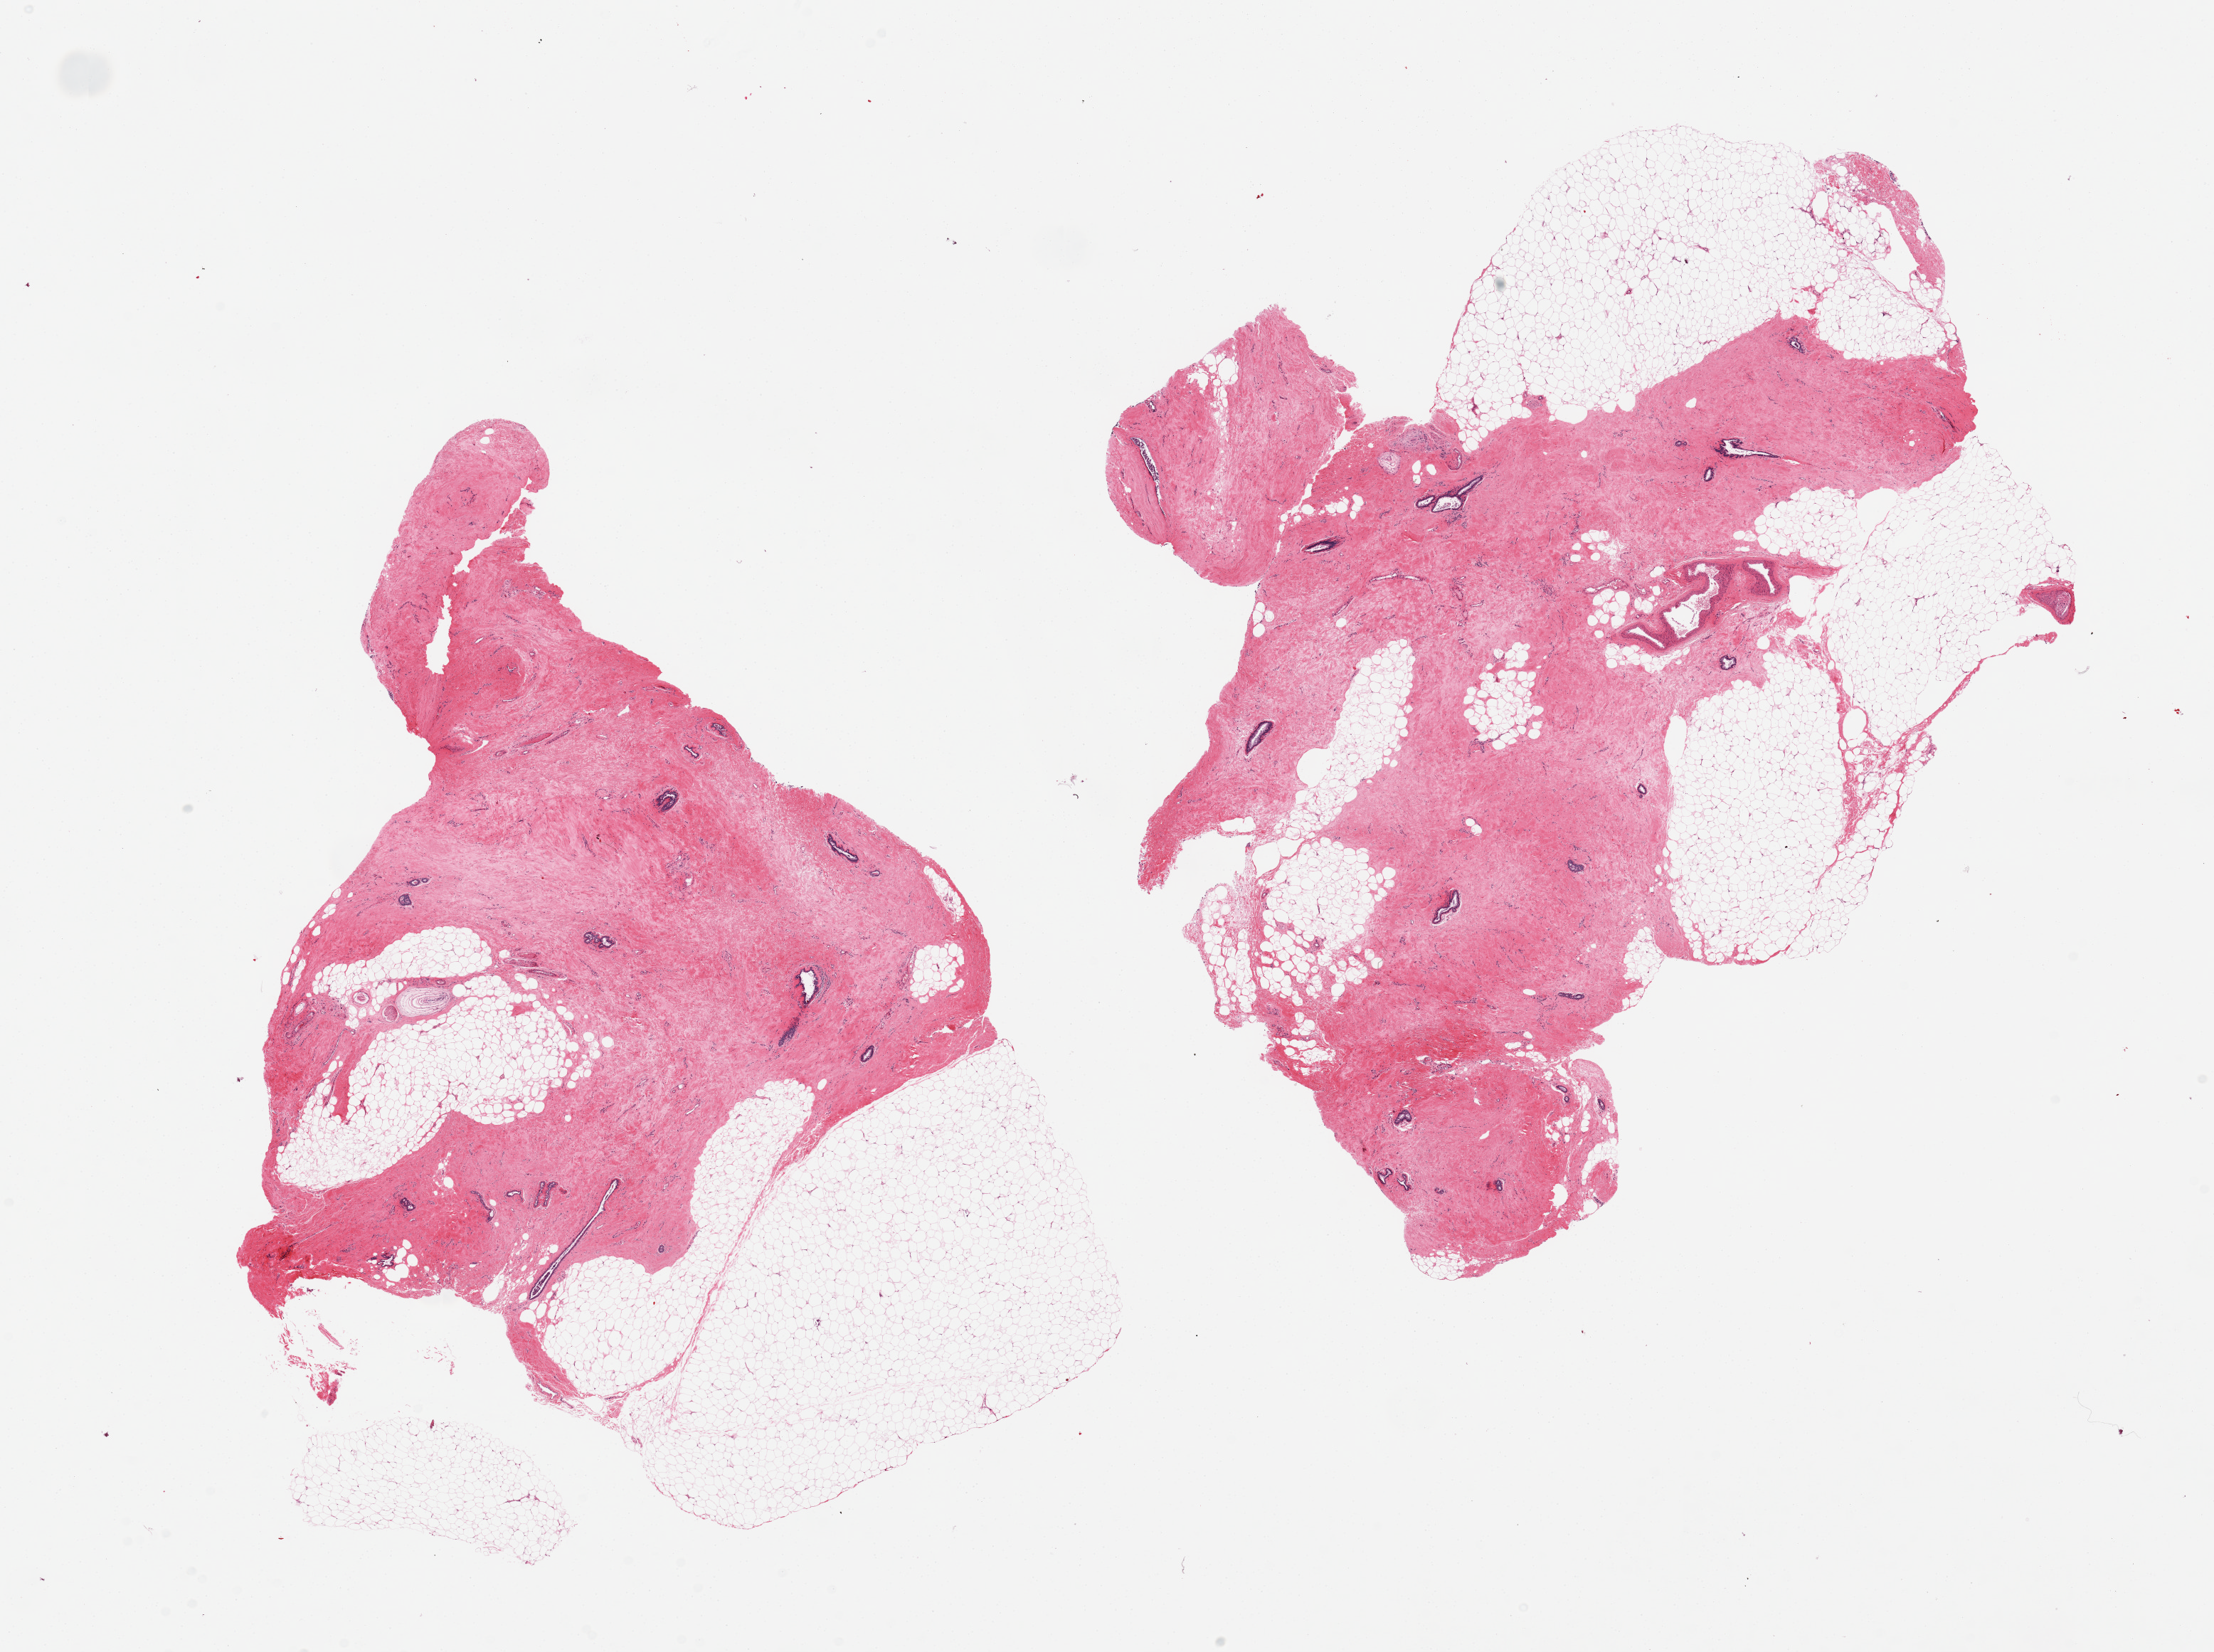
Digitized haematoxylin and eosin-stained section, brightfield, shown as a low-resolution overview of the whole scanned area (about 24.6 x 18.4 mm). PAXgene-fixed, paraffin-embedded tissue. Section of breast (target tissue). Donor tissue sample. Male donor.
Reviewer comment on this tissue sample: 2 pieces, gynecomastoid change, pacinian corpuscles, 30% fat.